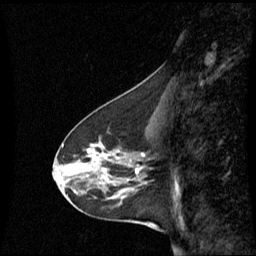
Breast MRI (dynamic contrast-enhanced), one sagittal slice; slice 27 of 60 in the series (ordered by position); dynamic contrast-enhanced series, image 2 of 3 at this slice position (ordered by acquisition); 1.5 T; TE 4.2 ms, TR 8.4 ms; 2.2 mm slice thickness; 256 × 256 image matrix. Patient: female, 45 years. Case-level facts recorded for this patient, not image findings: setting: breast cancer imaged before/during neoadjuvant chemotherapy; receptor status: HR-positive, HER2-negative.
Annotated regions visible in this slice (semi-automatic segmentation, software-assisted and operator-edited):
- analysis volume of interest (the breast-tissue region the enhancement analysis was run in; not a lesion): bounding box [x1, y1, x2, y2] px = [60, 126, 149, 215]
- tumour enhancement mask (voxels above the 70 % enhancement threshold inside the analysis volume of interest): [87, 148, 145, 173]